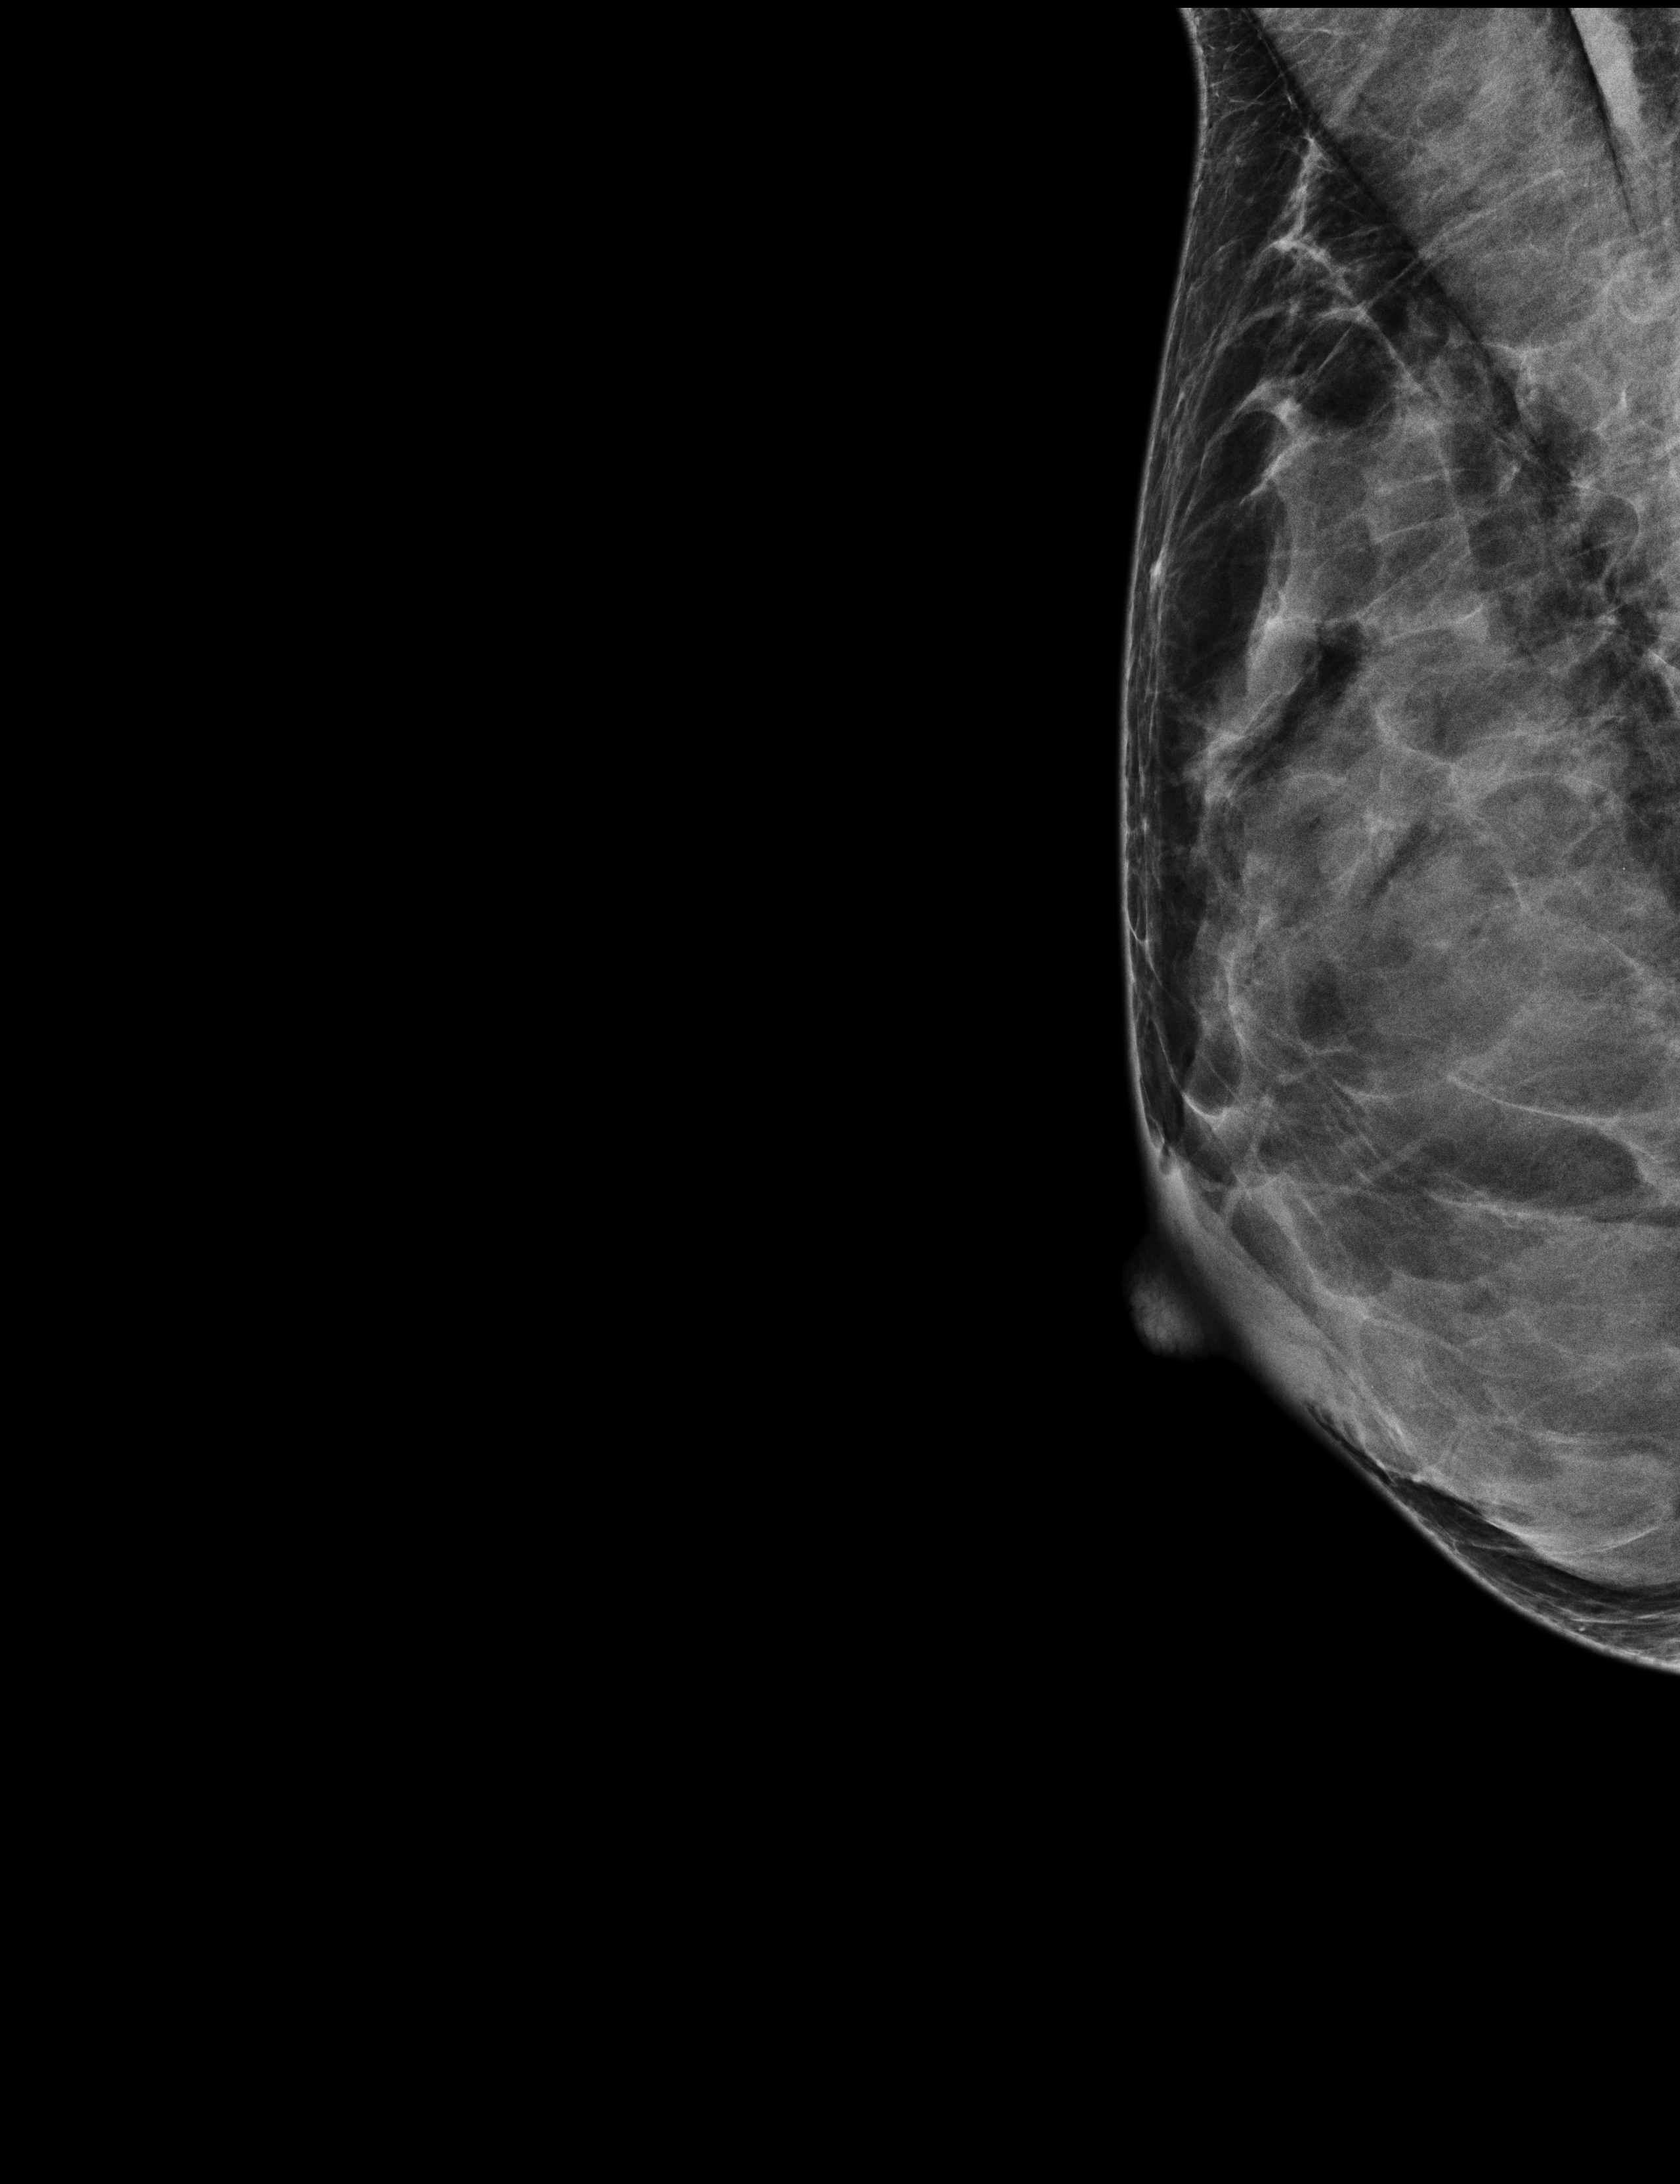
Full-field digital mammogram (FFDM), right breast, mediolateral oblique (MLO) view, screening examination, system: Selenia Dimensions. Female patient, age 42 years.
BI-RADS breast density category at the screening exam (both breasts, scale 1–4): 4. Final BI-RADS category for the screening round (tomosynthesis exam, both breasts): category 1. Recall: no recall after this screen.